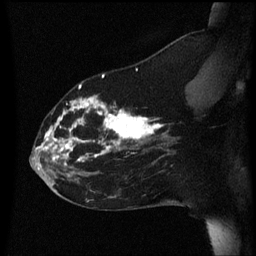
Breast MRI (dynamic contrast-enhanced), one sagittal slice; dynamic contrast-enhanced series, image 2 of 3 at this slice position (ordered by acquisition); 1.5 T; TE 4.2 ms, TR 8.4 ms; 2.2 mm slice thickness; 256 × 256 image matrix, field of view 200 × 200 mm. Female patient, age 35 years. From the clinical record (not read from this slice): setting: breast cancer imaged before/during neoadjuvant chemotherapy; receptor status: HER2-positive.
Outlined on this slice (semi-automatically segmented with operator editing):
- analysis volume of interest (the breast-tissue region the enhancement analysis was run in; not a lesion): bounding box (x1, y1, x2, y2) in pixels: (30, 72, 178, 173)
- tumour enhancement mask (voxels above the 70 % enhancement threshold inside the analysis volume of interest): (38, 74, 164, 163)